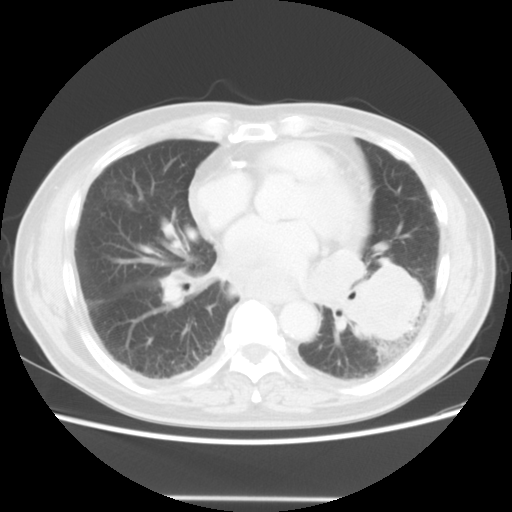
Chest CT, one axial slice. Slice 21 of 56 in the series (ordered by position). Reconstruction kernel STANDARD. 140 kVp. Lung window (W 1500 / L -600 HU). 5 mm slice thickness. 512 × 512 image matrix, field of view 360 × 360 mm. Patient: male, 66 years. Case-level facts recorded for this patient, not image findings: clinical TNM (as recorded): T4 N3 M0.
Structures marked on this image (rectangle marked by the reading radiologist):
- lung tumour (recorded histology: small cell carcinoma): bounding box [x1, y1, x2, y2] px = [342, 259, 428, 347]